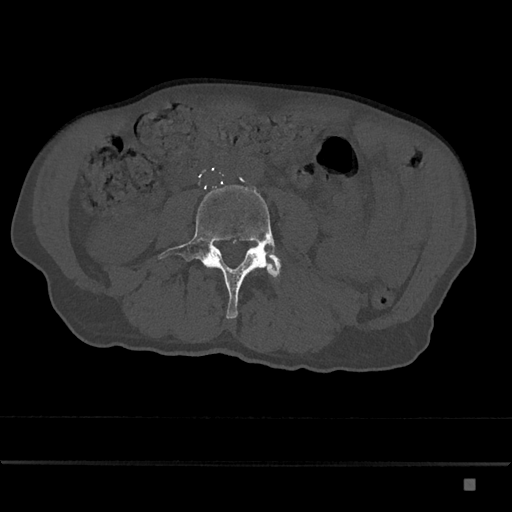
CT including the spine, one axial slice. Slice 342 of 797 in the series (ordered by position). Reconstruction kernel Br40s/3. Bone window (W 1800 / L 400 HU). 0.5 mm slice thickness. 512 × 512 image matrix. Male patient, age 72 years. From the clinical record (not read from this slice): primary cancer: prostate.
Annotated regions visible in this slice (semi-automatic segmentation, software-assisted and operator-edited):
- L4 vertebra: bounding box [x1, y1, x2, y2] px = [158, 185, 280, 319]
- L5 vertebra: [272, 256, 281, 269]